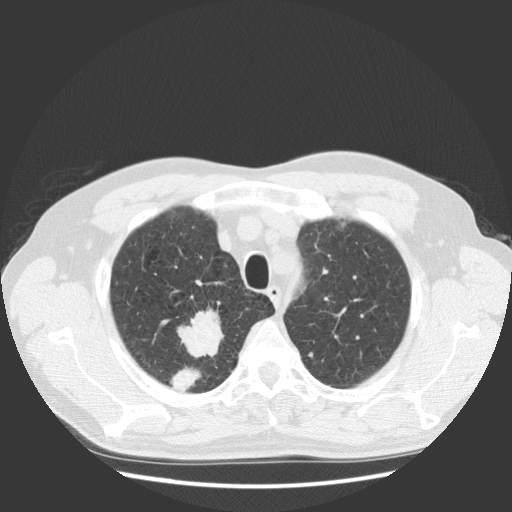
Low-dose screening chest CT, axial slice. Baseline screening round. Lung window (W 1500 / L -600 HU). 2.5 mm slice thickness. Slice 104 of 131 in the series. Male, age 63 years at enrolment. Current smoker at enrolment.
Expert-annotated lung lesion, bounding box <163,313,235,381> (left, top, right, bottom; pixels). The screening reader recorded 2 non-calcified nodules or masses ≥4 mm on this exam (right upper lobe, right upper lobe); which of them this box marks is not recorded. Later outcome: lung cancer diagnosed 30 days after this screen — squamous cell carcinoma, NOS, right upper lobe, stage IIIB (AJCC 6th edition), 35 mm at pathology.